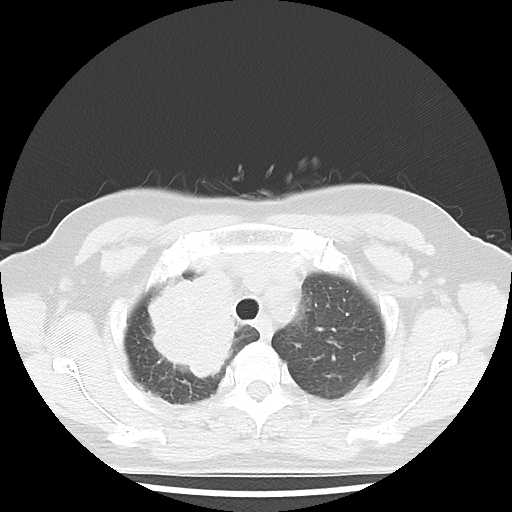
Chest CT, one axial slice. Position 35 of 43 along the scan axis. 100 kVp. Lung window (W 1500 / L -600 HU). 5 mm slice thickness. 512 × 512 image matrix, field of view 316 × 316 mm. Patient: female, 62 years. Case-level facts recorded for this patient, not image findings: clinical TNM (as recorded): T3 N0 M0.
Outlined on this slice (rectangle marked by the reading radiologist):
- lung tumour (recorded histology: small cell carcinoma): bounding box (x1, y1, x2, y2) in pixels: (144, 255, 244, 389)